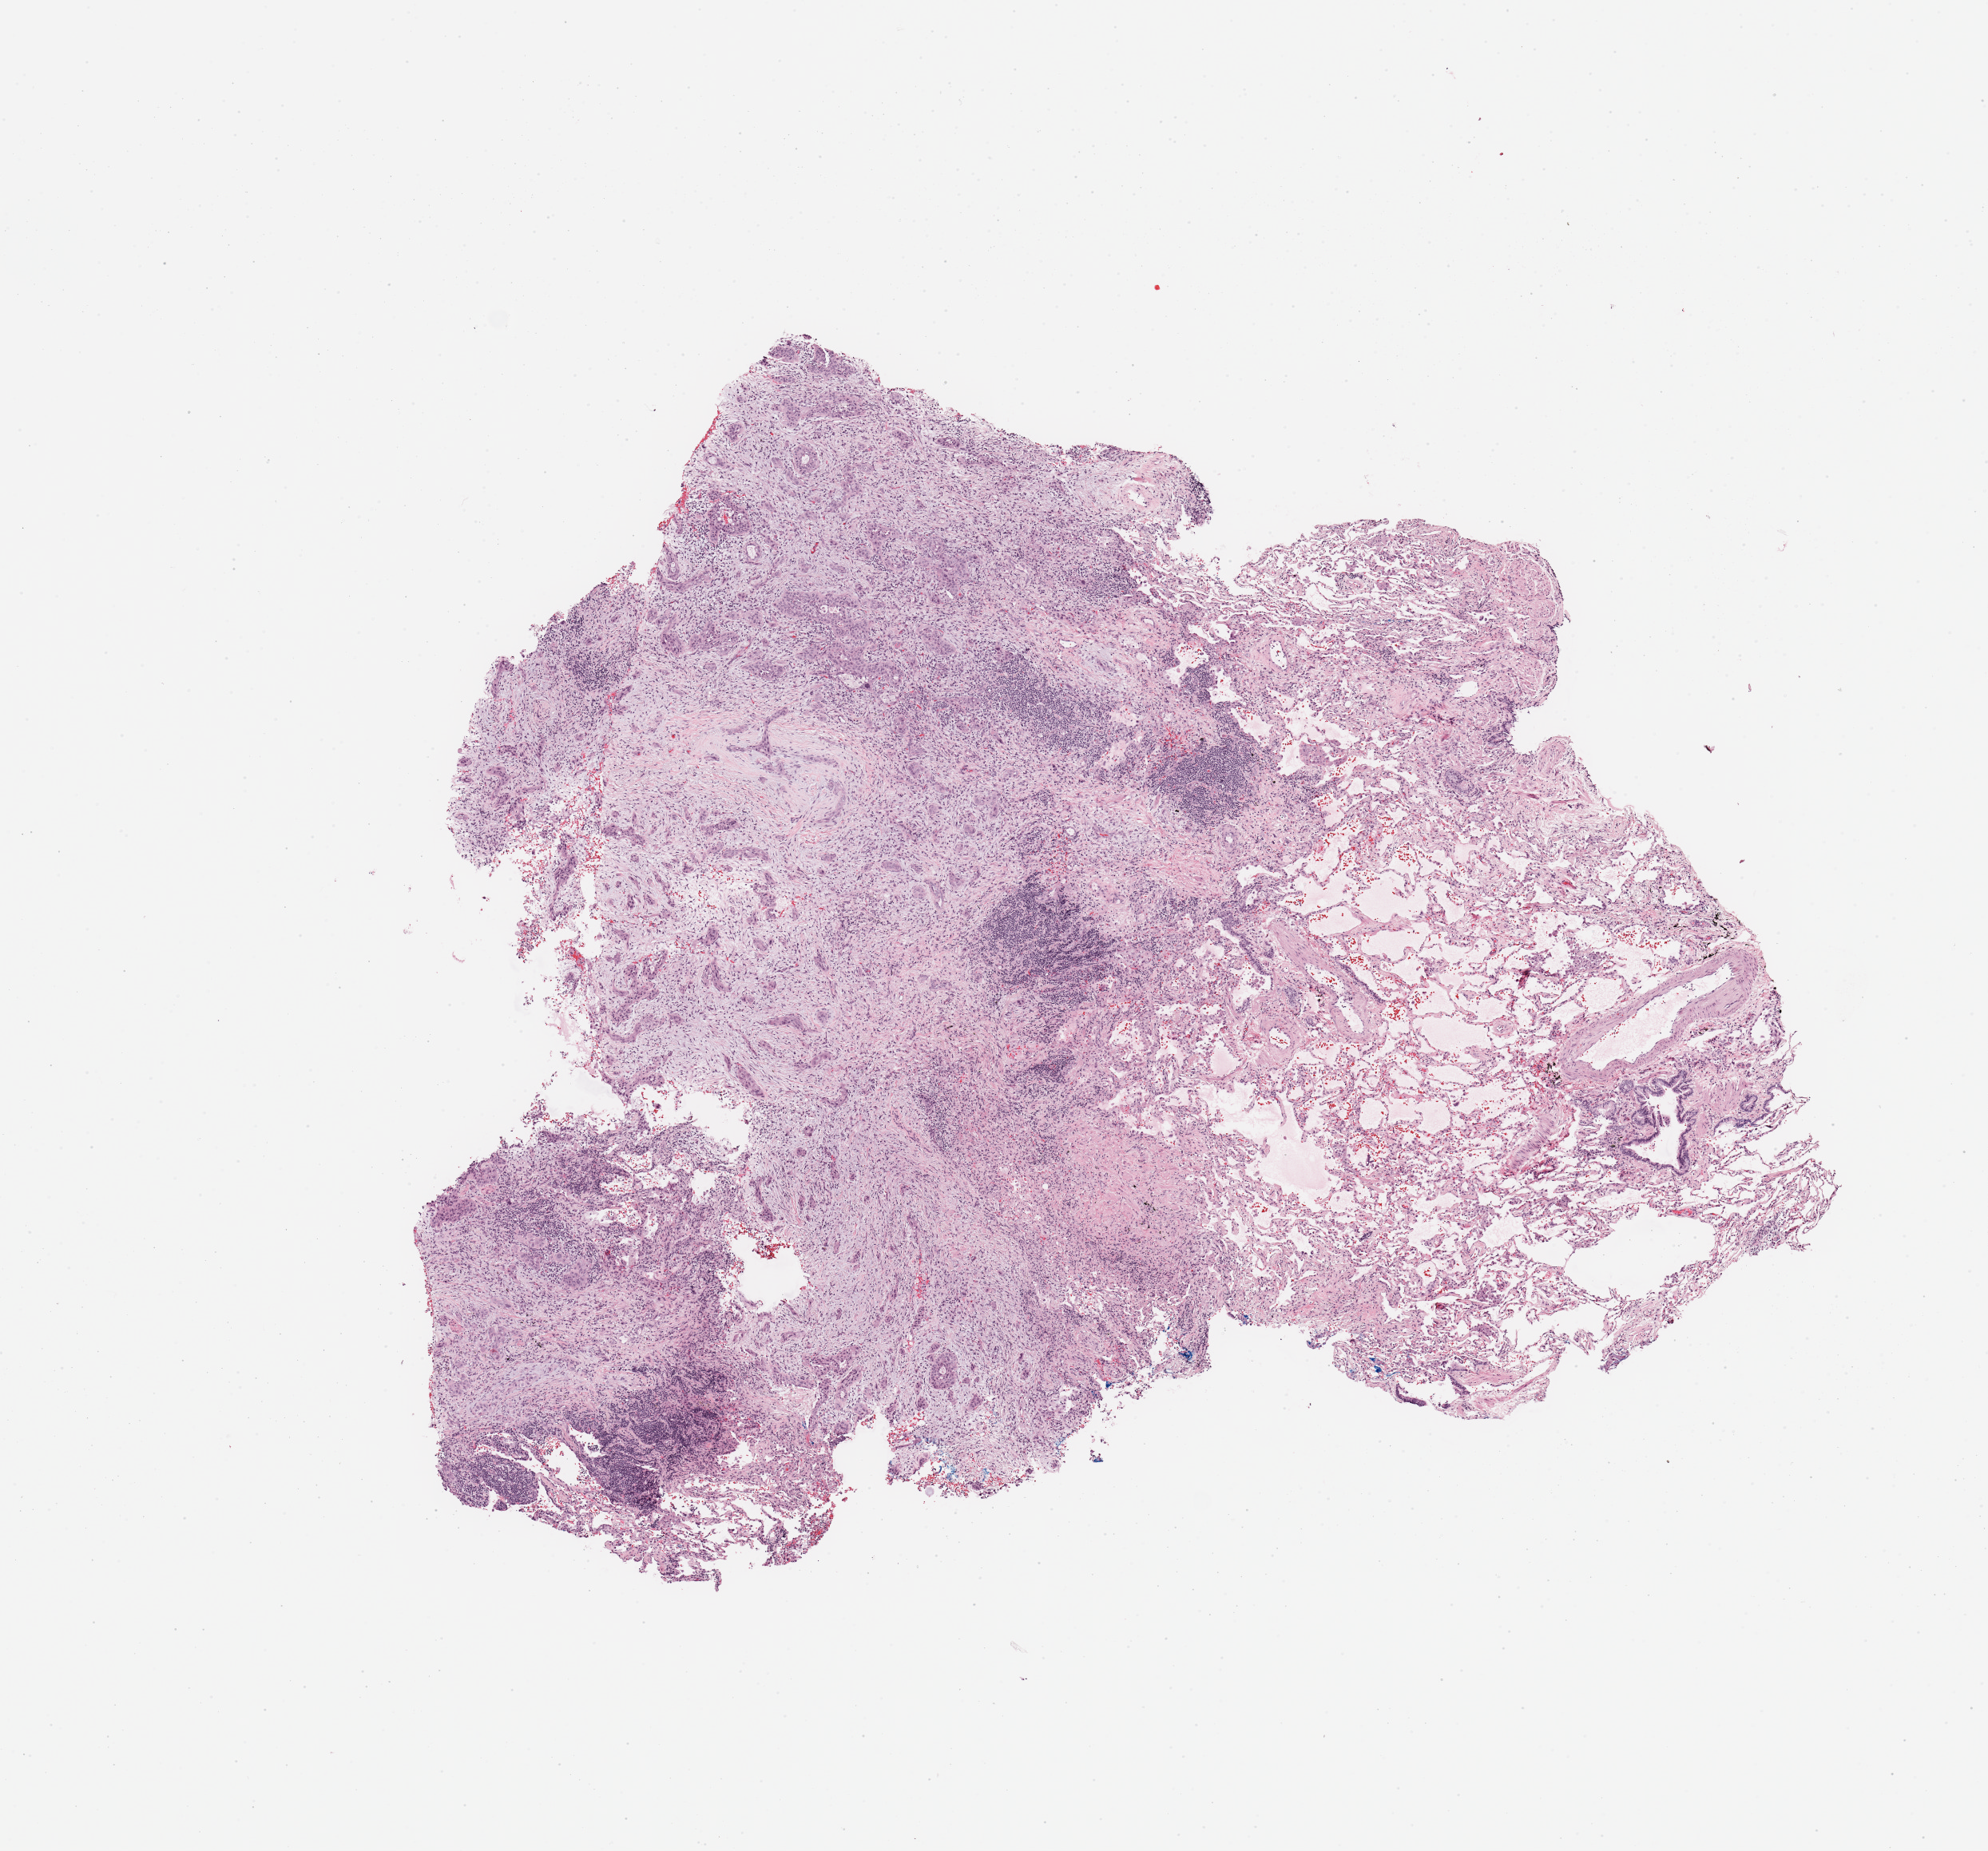
H&E whole-slide image — shown as a low-resolution overview of the whole scanned area (about 9.8 x 9.2 mm); tumour tissue sample, lung. Patient: male, age 68 years. Histologic grade: G3 (poorly differentiated).
- primary tumour site (as recorded): left lower lobe
- histologic diagnosis: Squamous cell carcinoma, NOS
- AJCC pathologic stage: IB